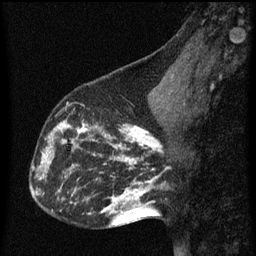
Breast MRI (dynamic contrast-enhanced), one sagittal slice; position 24 of 60 along the scan axis; dynamic contrast-enhanced series, image 2 of 3 at this slice position (ordered by acquisition); 1.5 T; TE 4.2 ms, TR 8 ms; 2 mm slice thickness; 256 × 256 image matrix, field of view 180 × 180 mm. Patient: female, 43 years.
Structures marked on this image (semi-automatically segmented with operator editing):
- analysis volume of interest (the breast-tissue region the enhancement analysis was run in; not a lesion): bounding box <53,104,101,155> (left, top, right, bottom; pixels)
- tumour enhancement mask (voxels above the 70 % enhancement threshold inside the analysis volume of interest): <53,104,98,155>